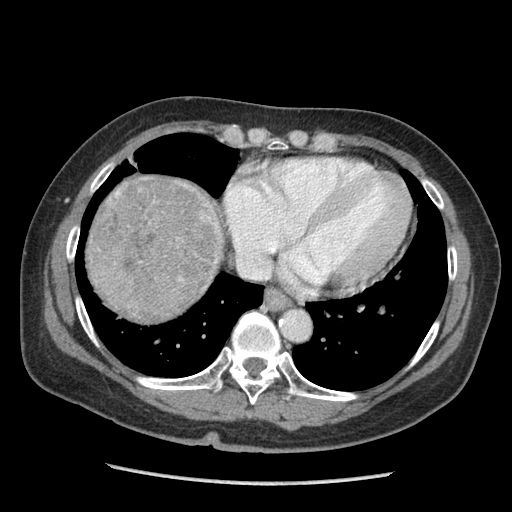
Contrast-enhanced abdominal CT (liver protocol), one axial slice; slice 89 of 105 in the series (ordered by position); 140 kVp; soft-tissue window (W 400 / L 40 HU); 2.5 mm slice thickness; 512 × 512 image matrix, field of view 340 × 340 mm. From the clinical record (not read from this slice): diagnosis: hepatocellular carcinoma (patient treated with transarterial chemoembolisation; whether this scan precedes or follows treatment is not stated here); TNM stage (as recorded): Stage-I; Child-Pugh class: A.
Annotated regions visible in this slice (semi-automatically segmented with operator editing):
- liver parenchyma outside the tumour (the mass and vessels are separate outlines, so this box may not span the whole liver): bounding box <86,174,219,316> (left, top, right, bottom; pixels)
- mass: <91,179,226,321>
- liver vessels: <116,192,119,194>